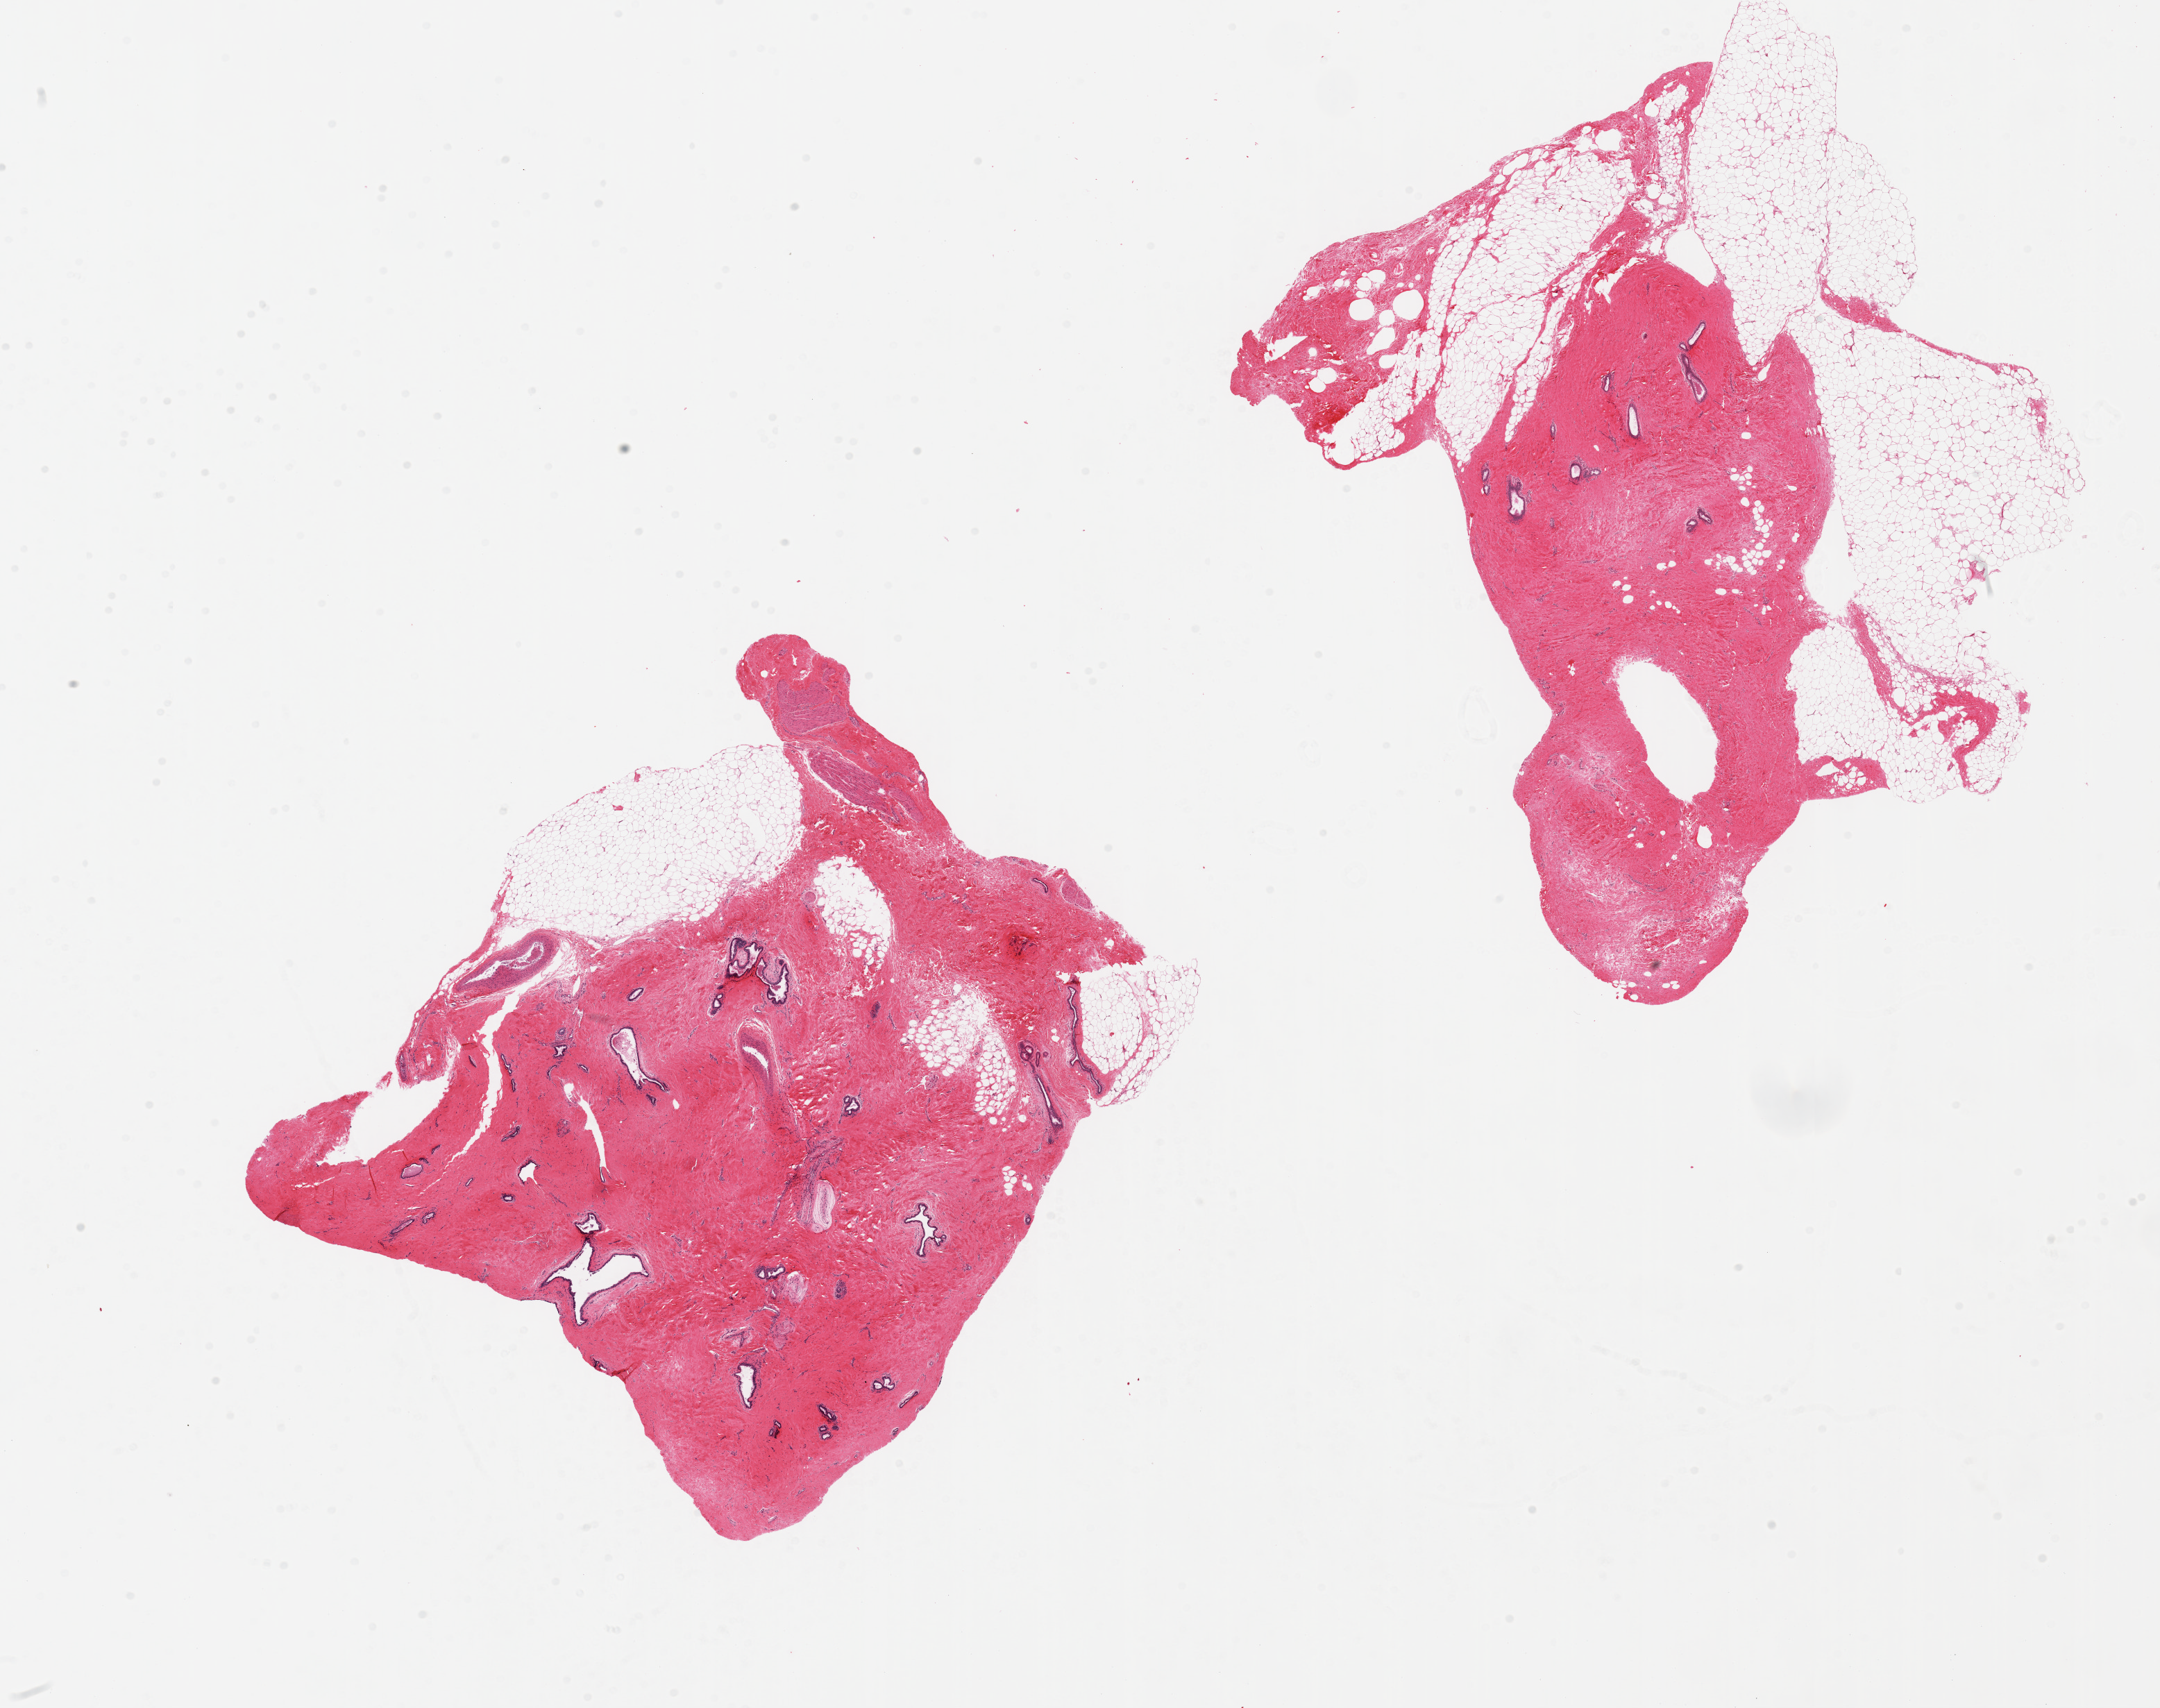
Whole-slide image, haematoxylin and eosin stain — shown as a low-resolution overview of the whole scanned area (about 24.6 x 19.5 mm, acquisition: 20x scan); PAXgene-fixed, paraffin-embedded tissue; target tissue: breast; tissue donor sample. Male donor.
- review note (as recorded): 2 pieces, gynecomastoid stromal/ductal hyperplasia; stroma, rep ducts